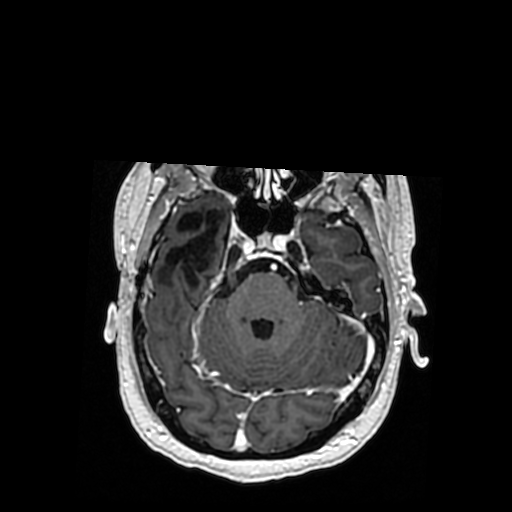
Brain MRI from a brain-tumour surgery series, one axial slice. Position 243 of 364 along the scan axis. T1-weighted post-contrast. 0.5 mm slice thickness. 512 × 512 image matrix. From the clinical record (not read from this slice): histopathology: Oligodendroglioma; WHO grade: 3; IDH mutation: yes; tumour location: Right Posterior Temporal Inferior Parietal.
Annotated regions visible in this slice (outlined manually by an expert reader):
- previous resection cavity: bounding box (x1, y1, x2, y2) in pixels: (160, 210, 228, 281)